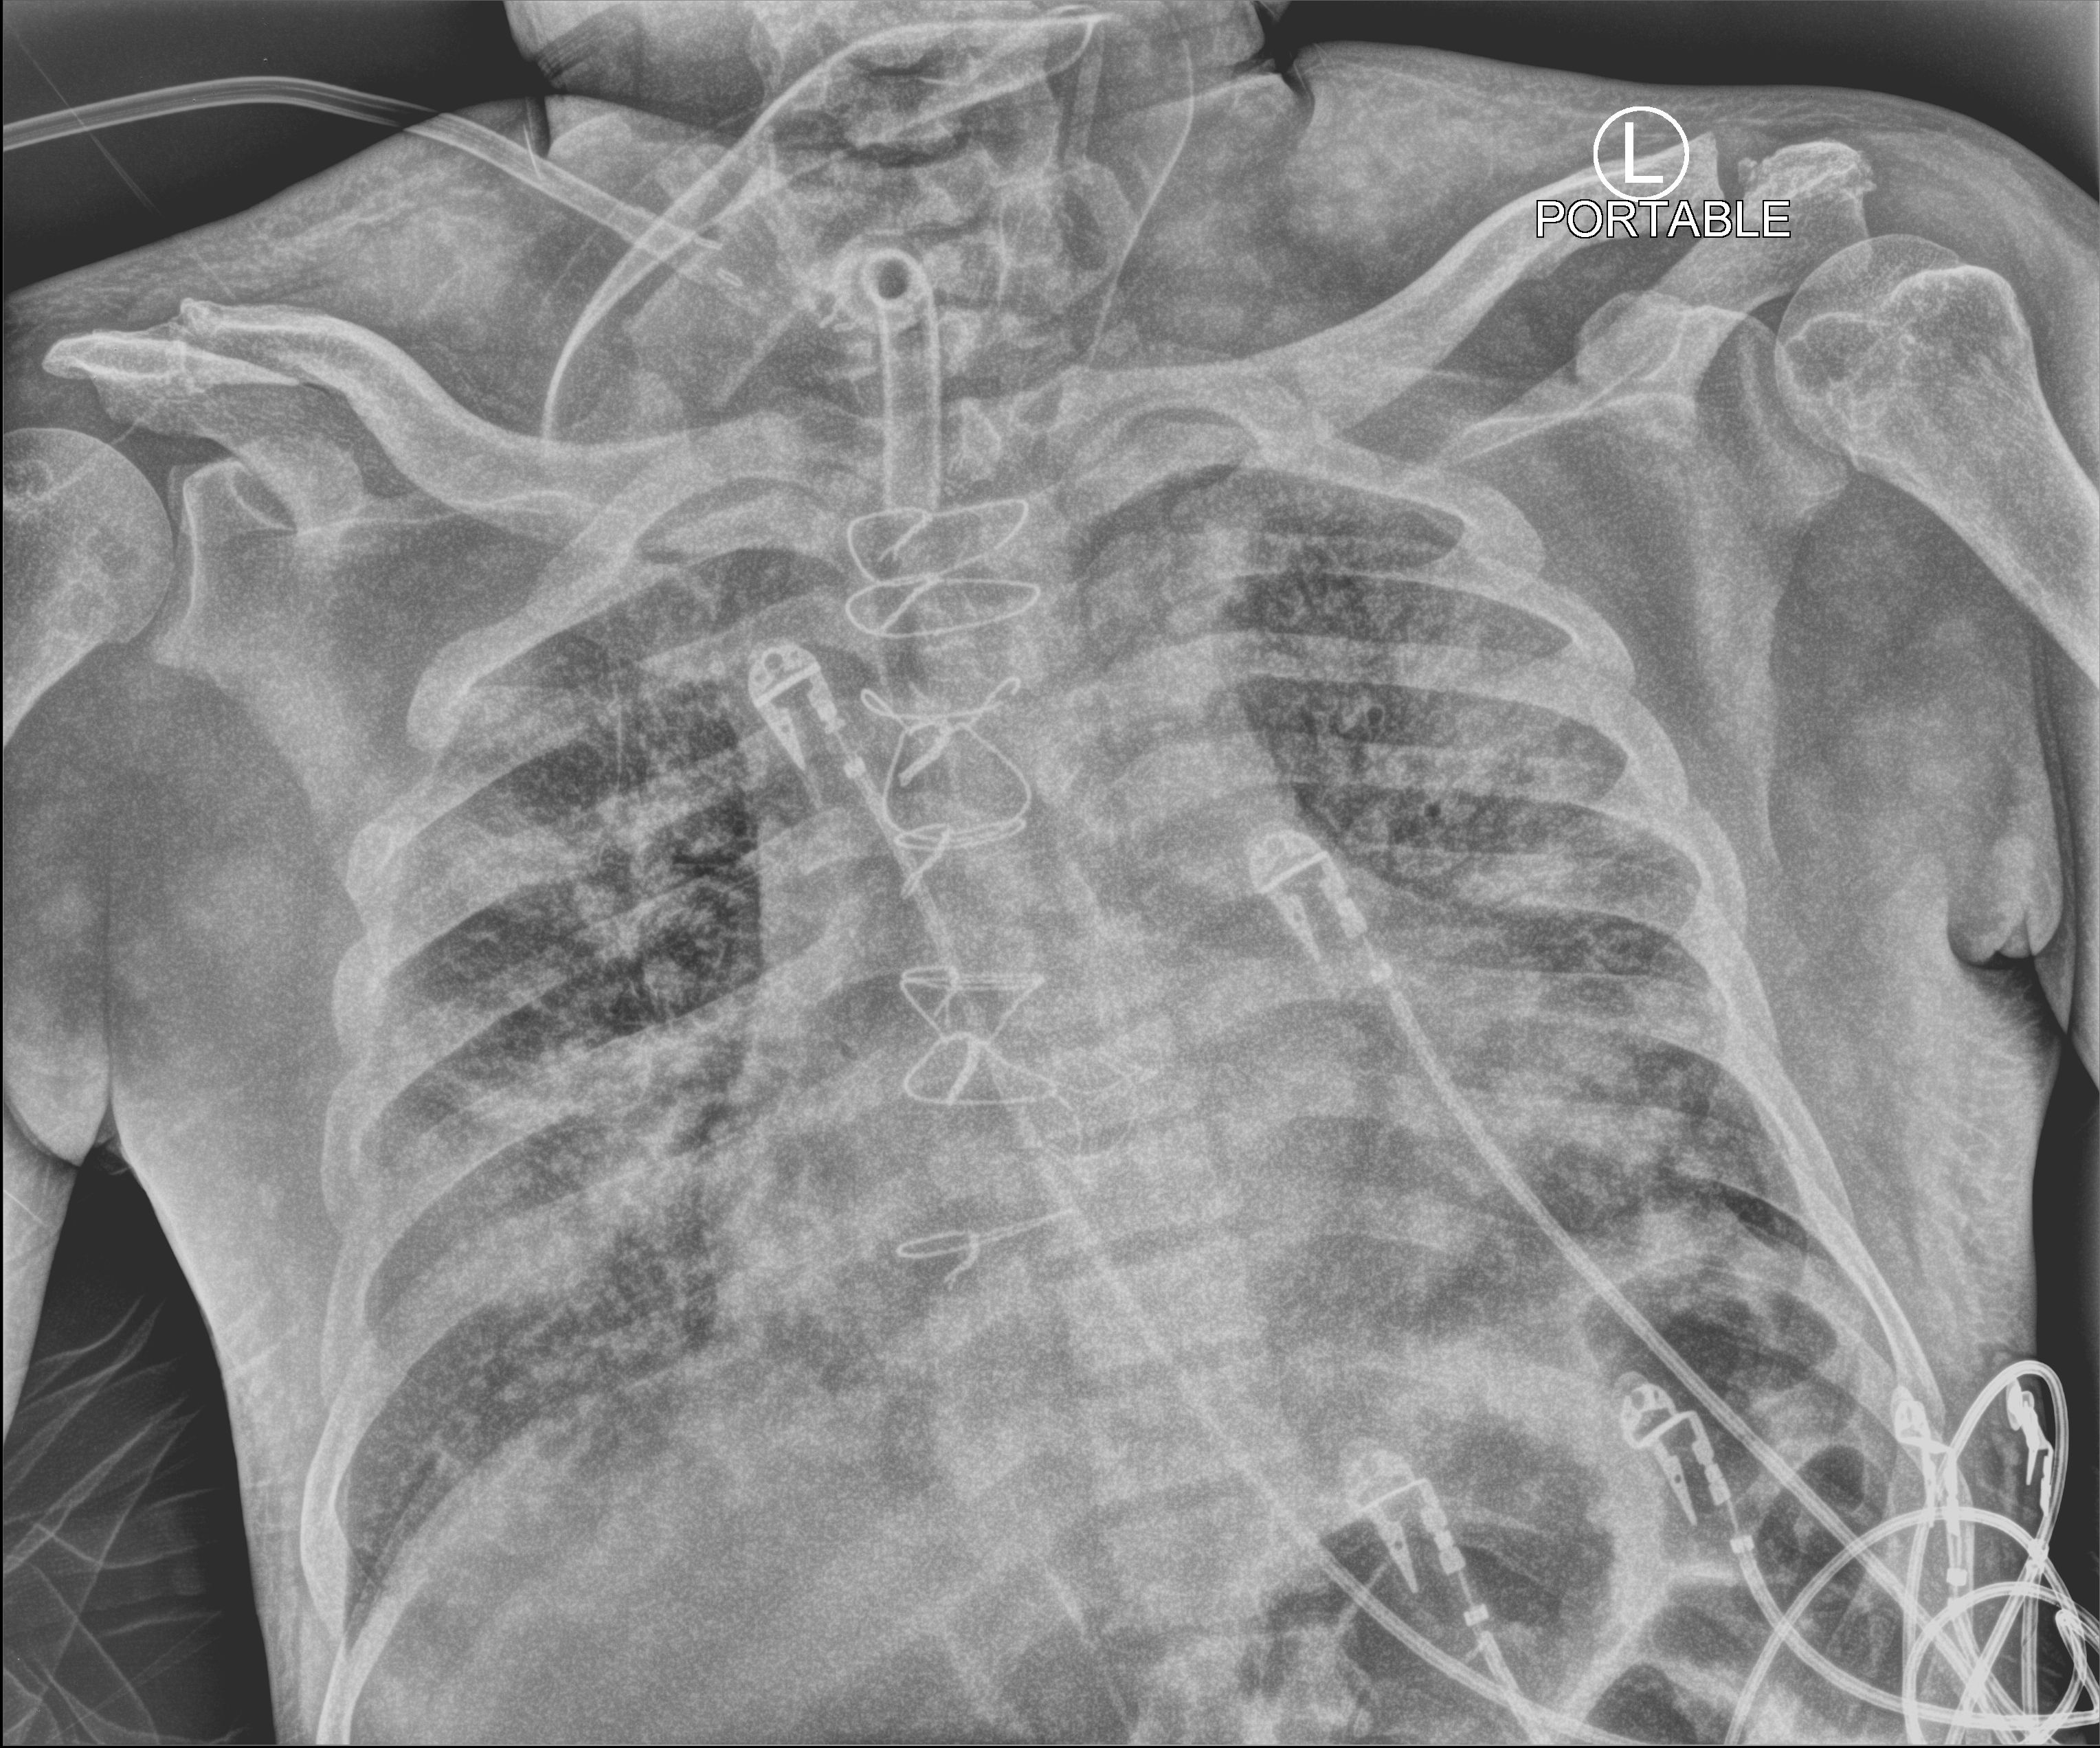
Portable chest radiograph; anteroposterior (AP) projection. Male patient hospitalised with COVID-19, age 60–74 years.
Hospital-stay facts (about this admission, not read from this image; timing relative to this image not recorded): length of hospital stay: 50 days; diabetes (admission record): no; mechanically ventilated during this hospital stay: yes.